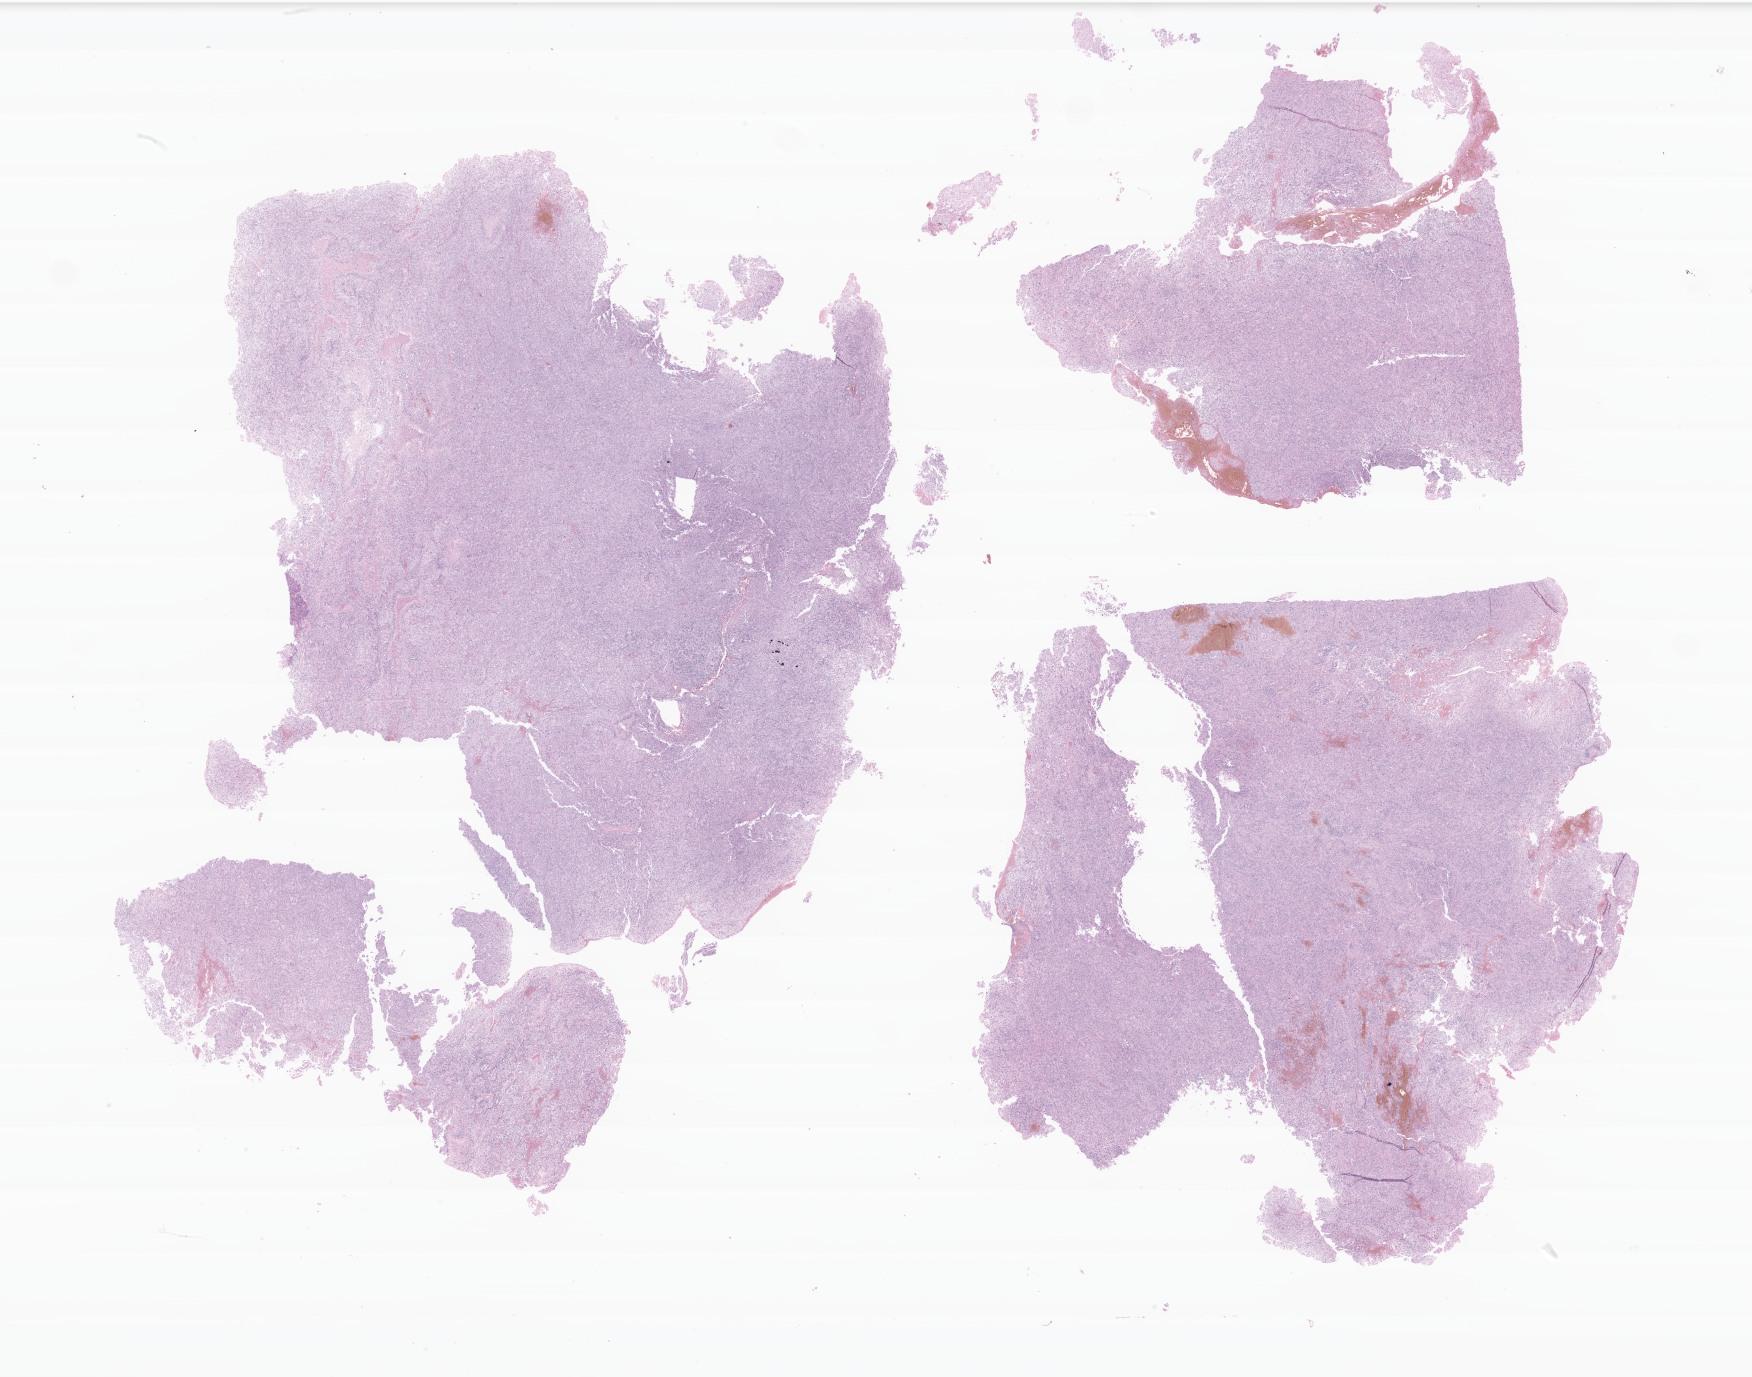
Digitized H&E-stained section of tumor tissue from the brain — a low-resolution overview of the entire scanned area, about 29.5 x 23.2 mm, formalin-fixed, paraffin-embedded (FFPE) tissue. Female patient, age 90 months (7 years 6 months).
Diagnosis: Glioblastoma, NOS.